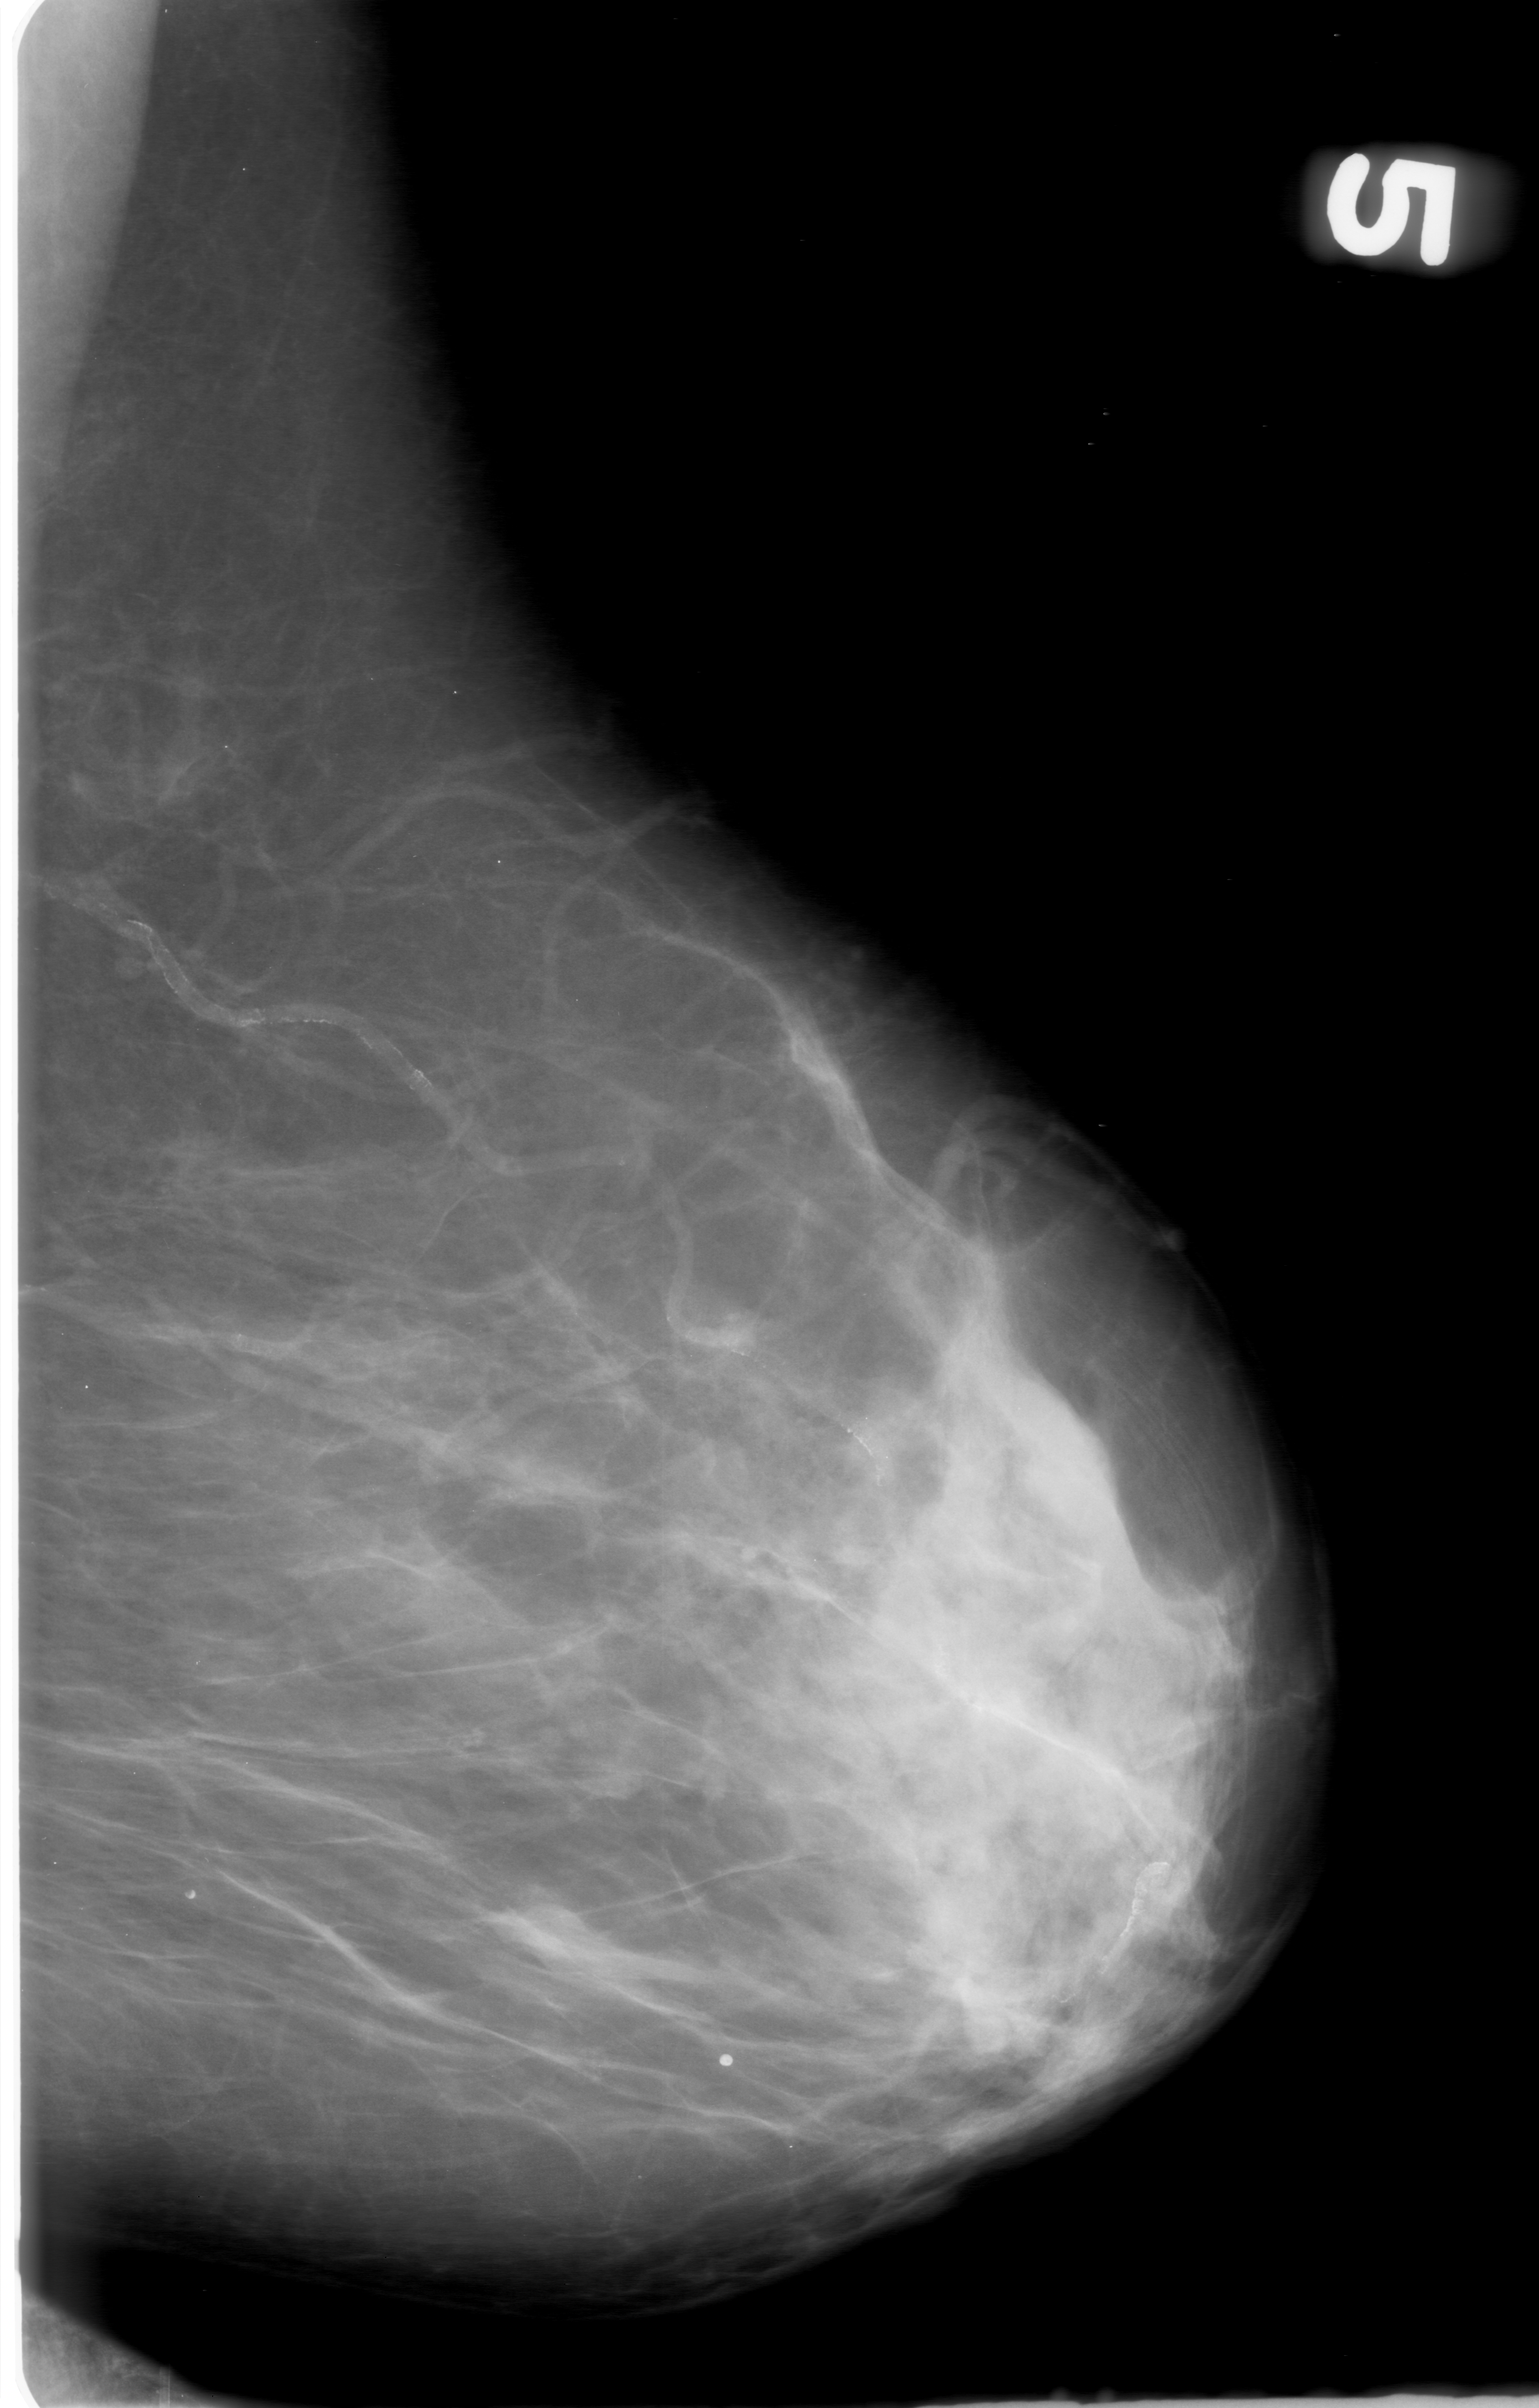
Scanned film-screen mammogram, left breast, mediolateral oblique (MLO) view, BI-RADS breast density category 2 (scale 1–4).
- Radiologist-marked abnormalities on this image: mass, shape round, margins obscured; BI-RADS assessment category 0 (incomplete: needs additional imaging); pathology result (as recorded, not read from the image): benign.